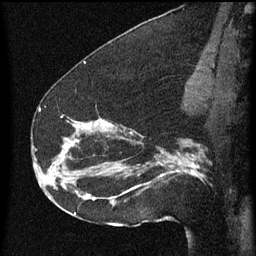
Breast MRI (dynamic contrast-enhanced), one sagittal slice; position 35 of 60 along the scan axis; dynamic contrast-enhanced series, image 2 of 3 at this slice position (ordered by acquisition); 1.5 T; TE 4.2 ms, TR 8 ms; 256 × 256 image matrix. Patient: female, 52 years.
Annotated regions visible in this slice (semi-automatically segmented with operator editing):
- analysis volume of interest (the breast-tissue region the enhancement analysis was run in; not a lesion): bounding box <54,112,178,207> (left, top, right, bottom; pixels)
- tumour enhancement mask (voxels above the 70 % enhancement threshold inside the analysis volume of interest): <61,116,178,201>